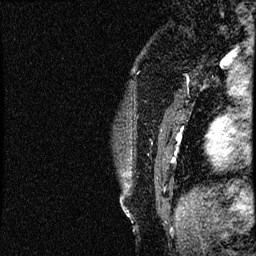
Breast MRI (dynamic contrast-enhanced), one sagittal slice; position 9 of 52 along the scan axis; dynamic contrast-enhanced study with each time point stored as its own series, time point 2 of 3 at this slice position (early post-contrast, ordered by acquisition time); 1.5 T; TE 4.2 ms, TR 17.6 ms; 2 mm slice thickness; 256 × 256 image matrix, field of view 200 × 200 mm. Patient: female, 49 years. Case-level facts recorded for this patient, not image findings: setting: breast cancer imaged before/during neoadjuvant chemotherapy; receptor status: HER2-positive.
Outlined on this slice (semi-automatically segmented with operator editing):
- analysis volume of interest (the breast-tissue region the enhancement analysis was run in; not a lesion): bounding box [x1, y1, x2, y2] px = [113, 65, 182, 175]
- tumour enhancement mask (voxels above the 100 % enhancement threshold inside the analysis volume of interest): [172, 159, 175, 163]